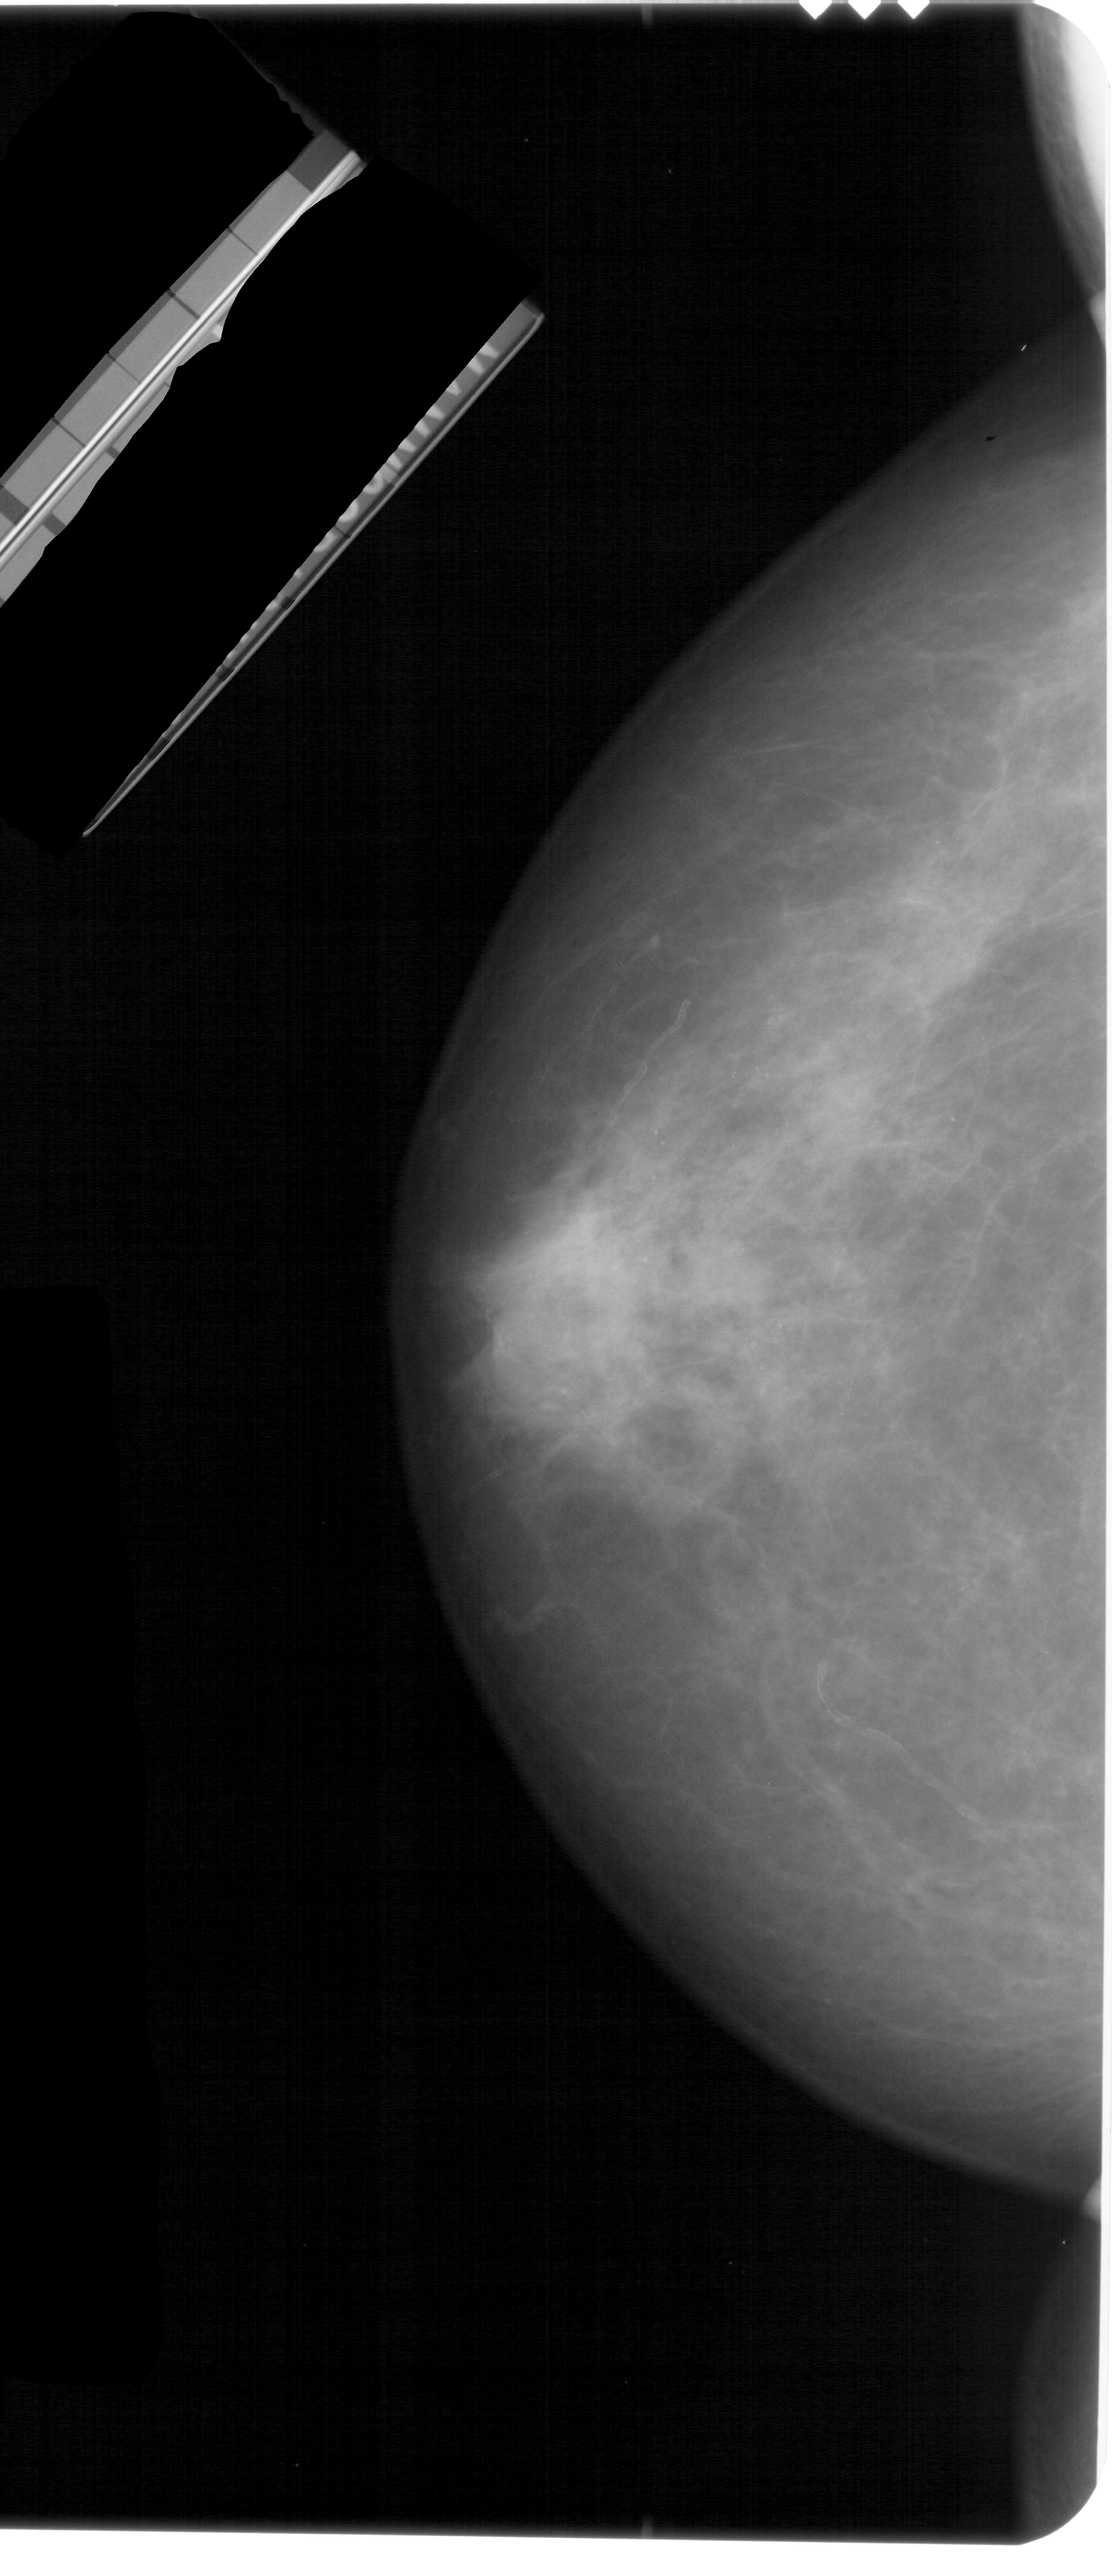
Mammogram (digitized film). Left breast. CC view. Breast composition: extremely dense (BI-RADS density category 4 of 4). 1112 × 2576 image matrix.
Expert-marked regions of interest on this film, with their recorded descriptors:
- calcifications, morphology punctate / amorphous, distribution regional; BI-RADS assessment category 4; subtlety rating 3 on a 1 (subtle) to 5 (obvious) scale; pathology result (as recorded, not read from the image): benign: bounding box [x1, y1, x2, y2] px = [469, 947, 831, 1500]